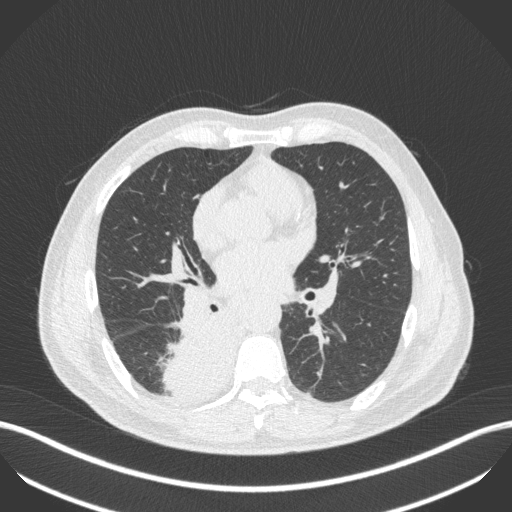
Chest CT, one axial slice; slice 240 of 451 in the series (ordered by position); reconstruction kernel B31f; lung window (W 1500 / L -600 HU); 1 mm slice thickness; 512 × 512 image matrix. Male patient, age 61 years. Case-level facts recorded for this patient, not image findings: clinical TNM (as recorded): T1 N0 M0; histopathological grade: G3.
Outlined on this slice (bounding box drawn by a radiologist):
- lung tumour (recorded histology: small cell carcinoma): bounding box [x1, y1, x2, y2] px = [158, 314, 235, 398]